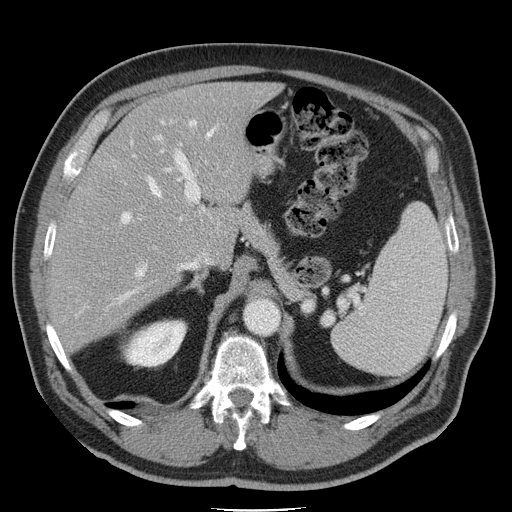
Contrast-enhanced abdominal CT, one axial slice; position 30 of 45 along the scan axis; soft-tissue window (W 400 / L 40 HU); 512 × 512 image matrix. Male patient, age 65 years. Case-level facts recorded for this patient, not image findings: diagnosis: colorectal cancer liver metastases, imaged before liver resection; multiple liver metastases: yes; largest metastasis: 4.9 cm; disease in both lobes: no.
Annotated regions visible in this slice (manually delineated by an expert):
- hepatic veins: bounding box [x1, y1, x2, y2] px = [82, 119, 219, 313]
- liver: [55, 83, 272, 346]
- planned liver remnant (the part of the liver to remain after resection): [102, 83, 272, 256]
- portal vein (with intrahepatic branches): [119, 120, 201, 280]